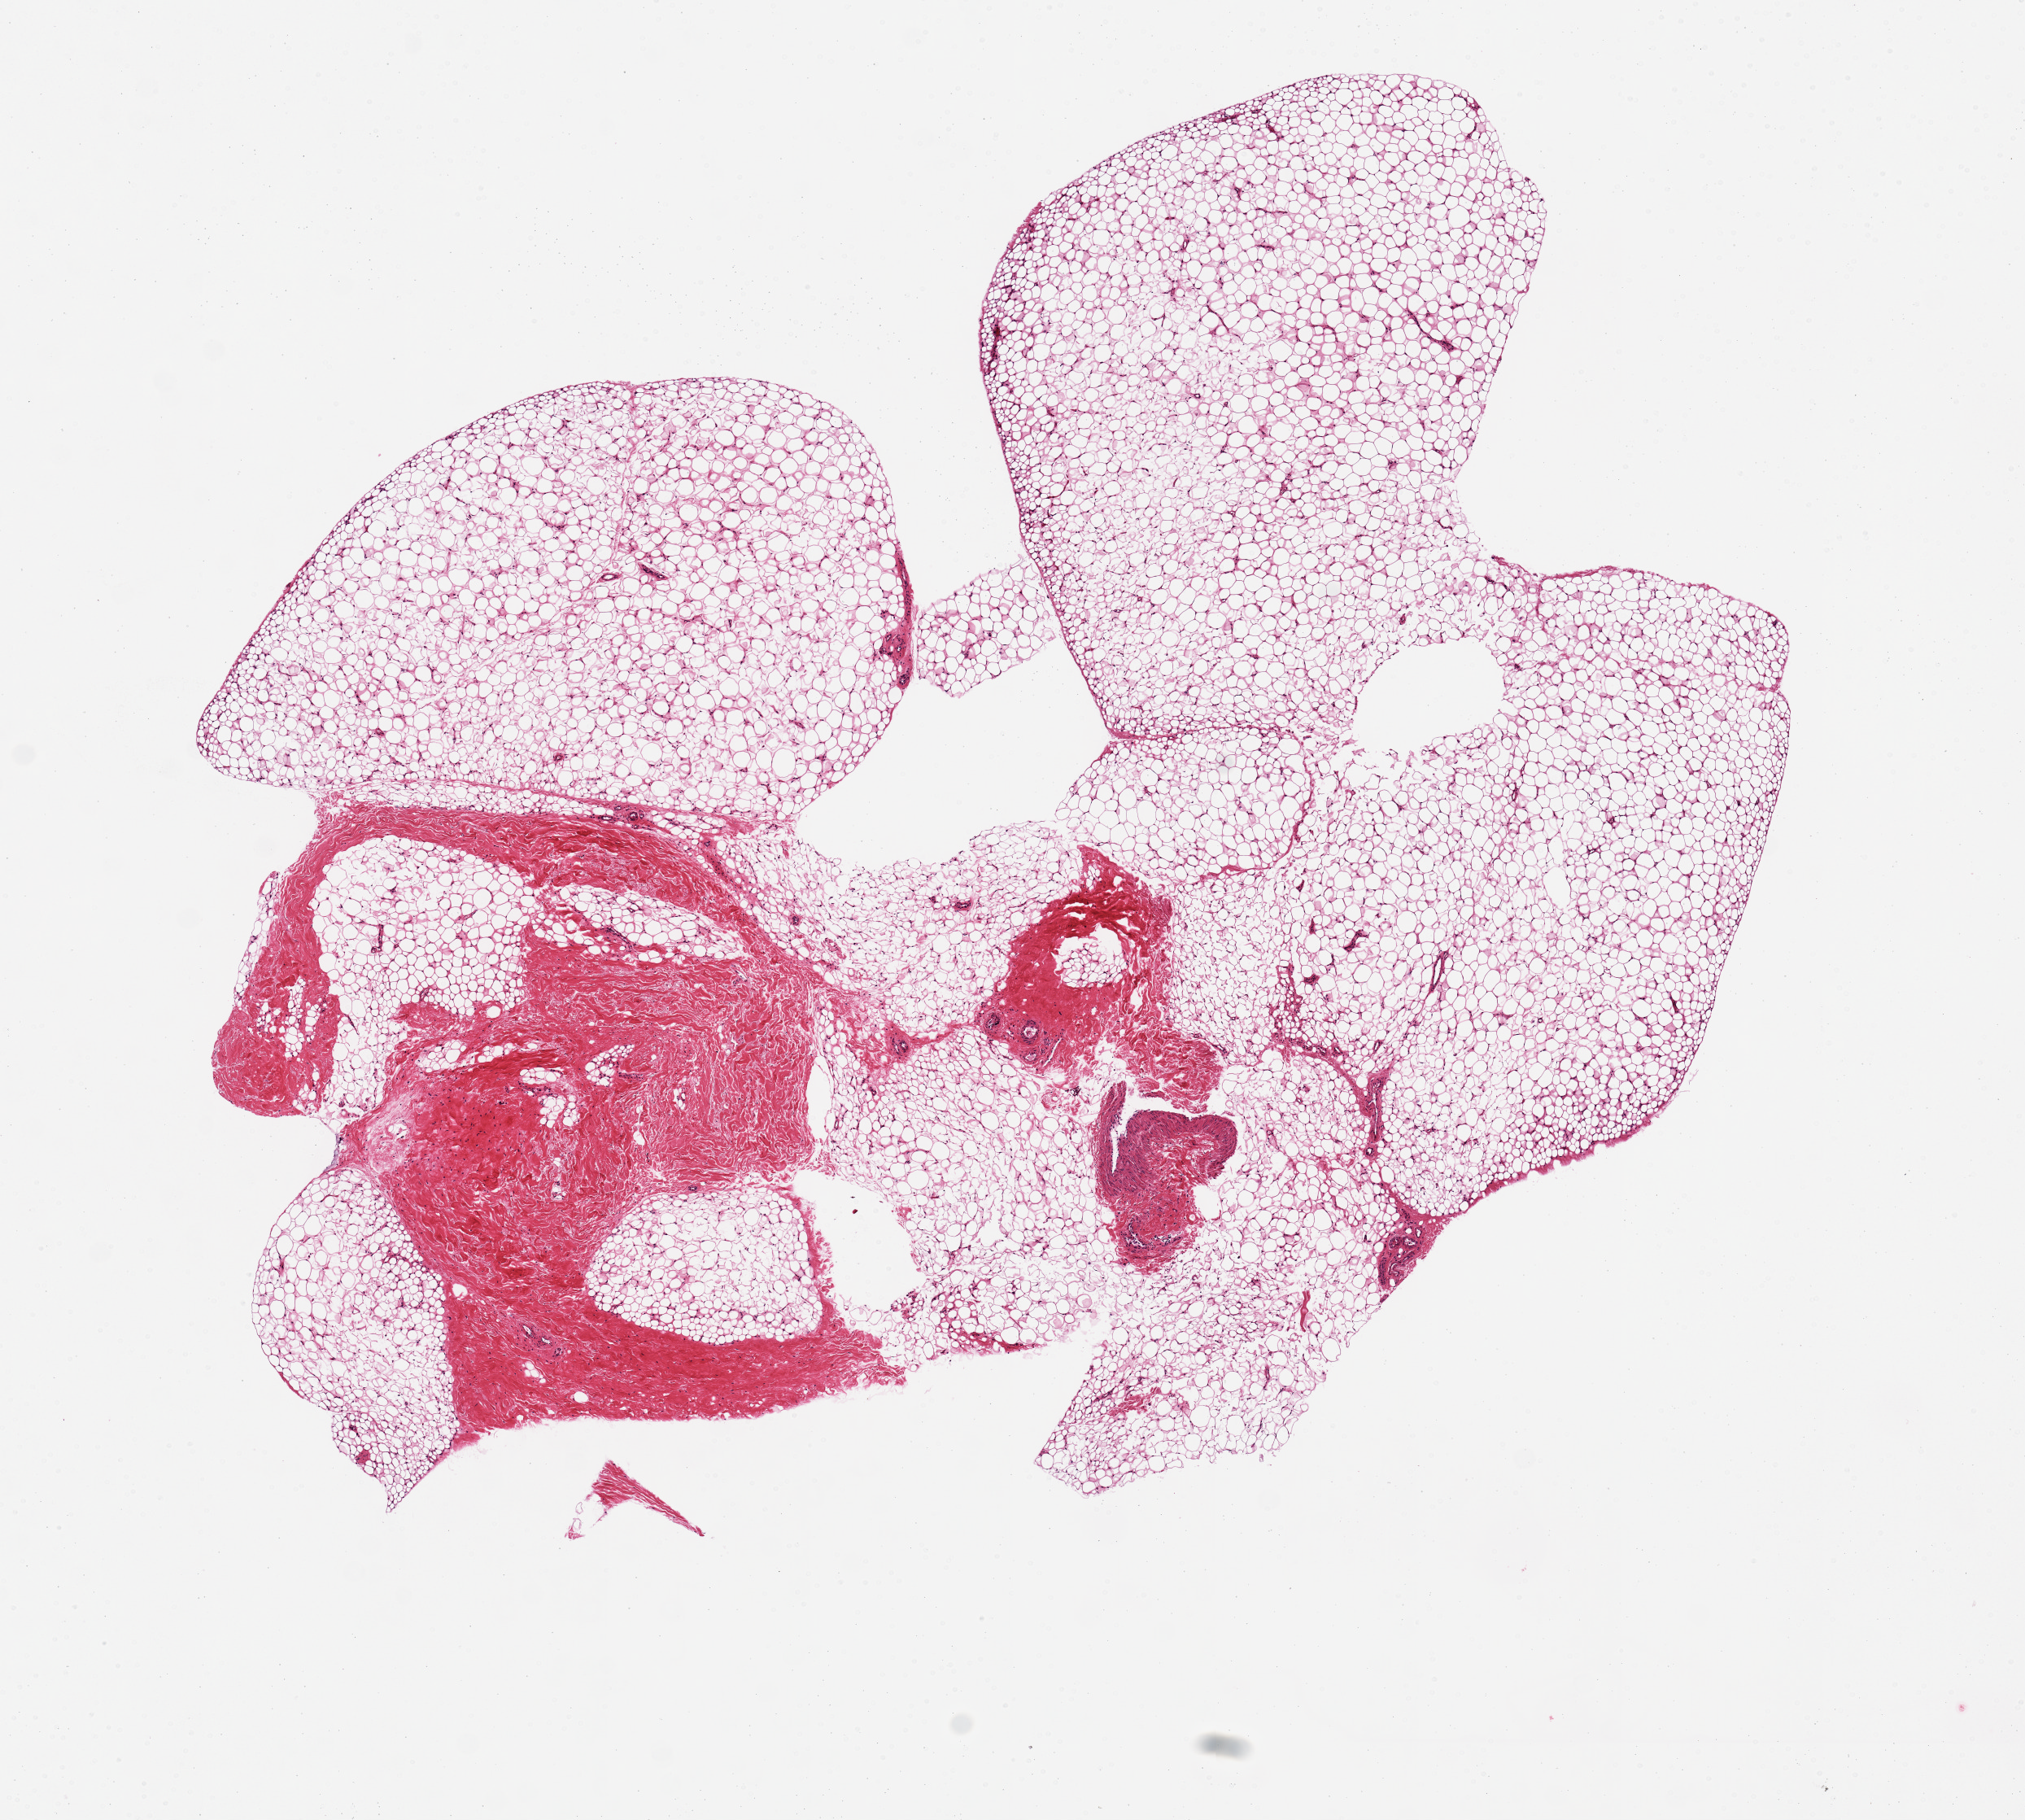
Whole-slide image, H&E stain — a low-resolution overview of the entire scanned area, about 9.8 x 8.8 mm, PAXgene-fixed, paraffin-embedded tissue, sampled site (target tissue): adipose tissue, tissue donor sample. Donor: male.
Review note (as recorded): 6.7x5.4. Well-fixed.